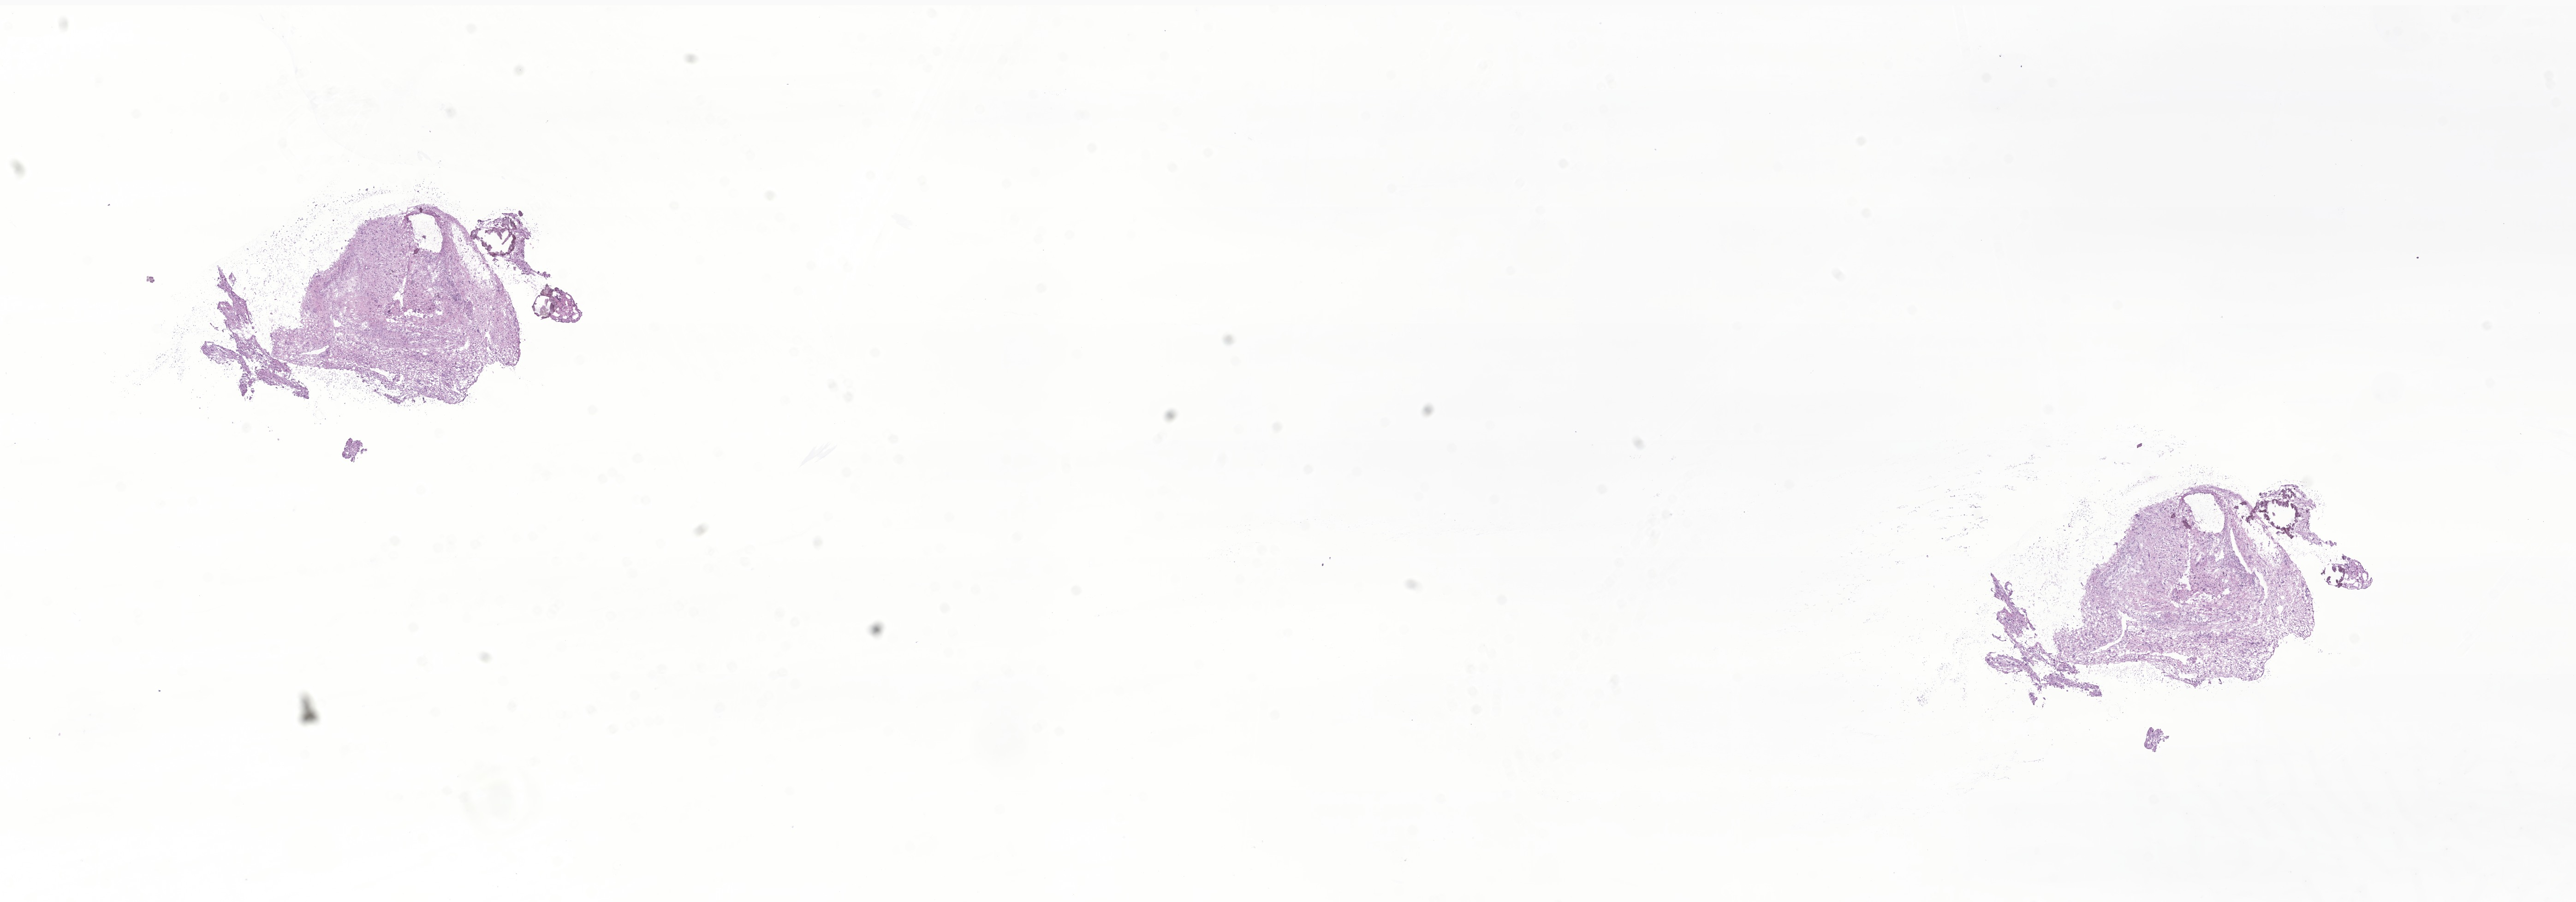
Hematoxylin and eosin (H&E) whole-slide image of tumor tissue from the occipital lobe — a low-resolution overview of the entire scanned area, about 23.5 x 8.2 mm. Frozen section. Patient female; age 164 months (13 years 8 months).
Diagnosis: Ganglioglioma, NOS.